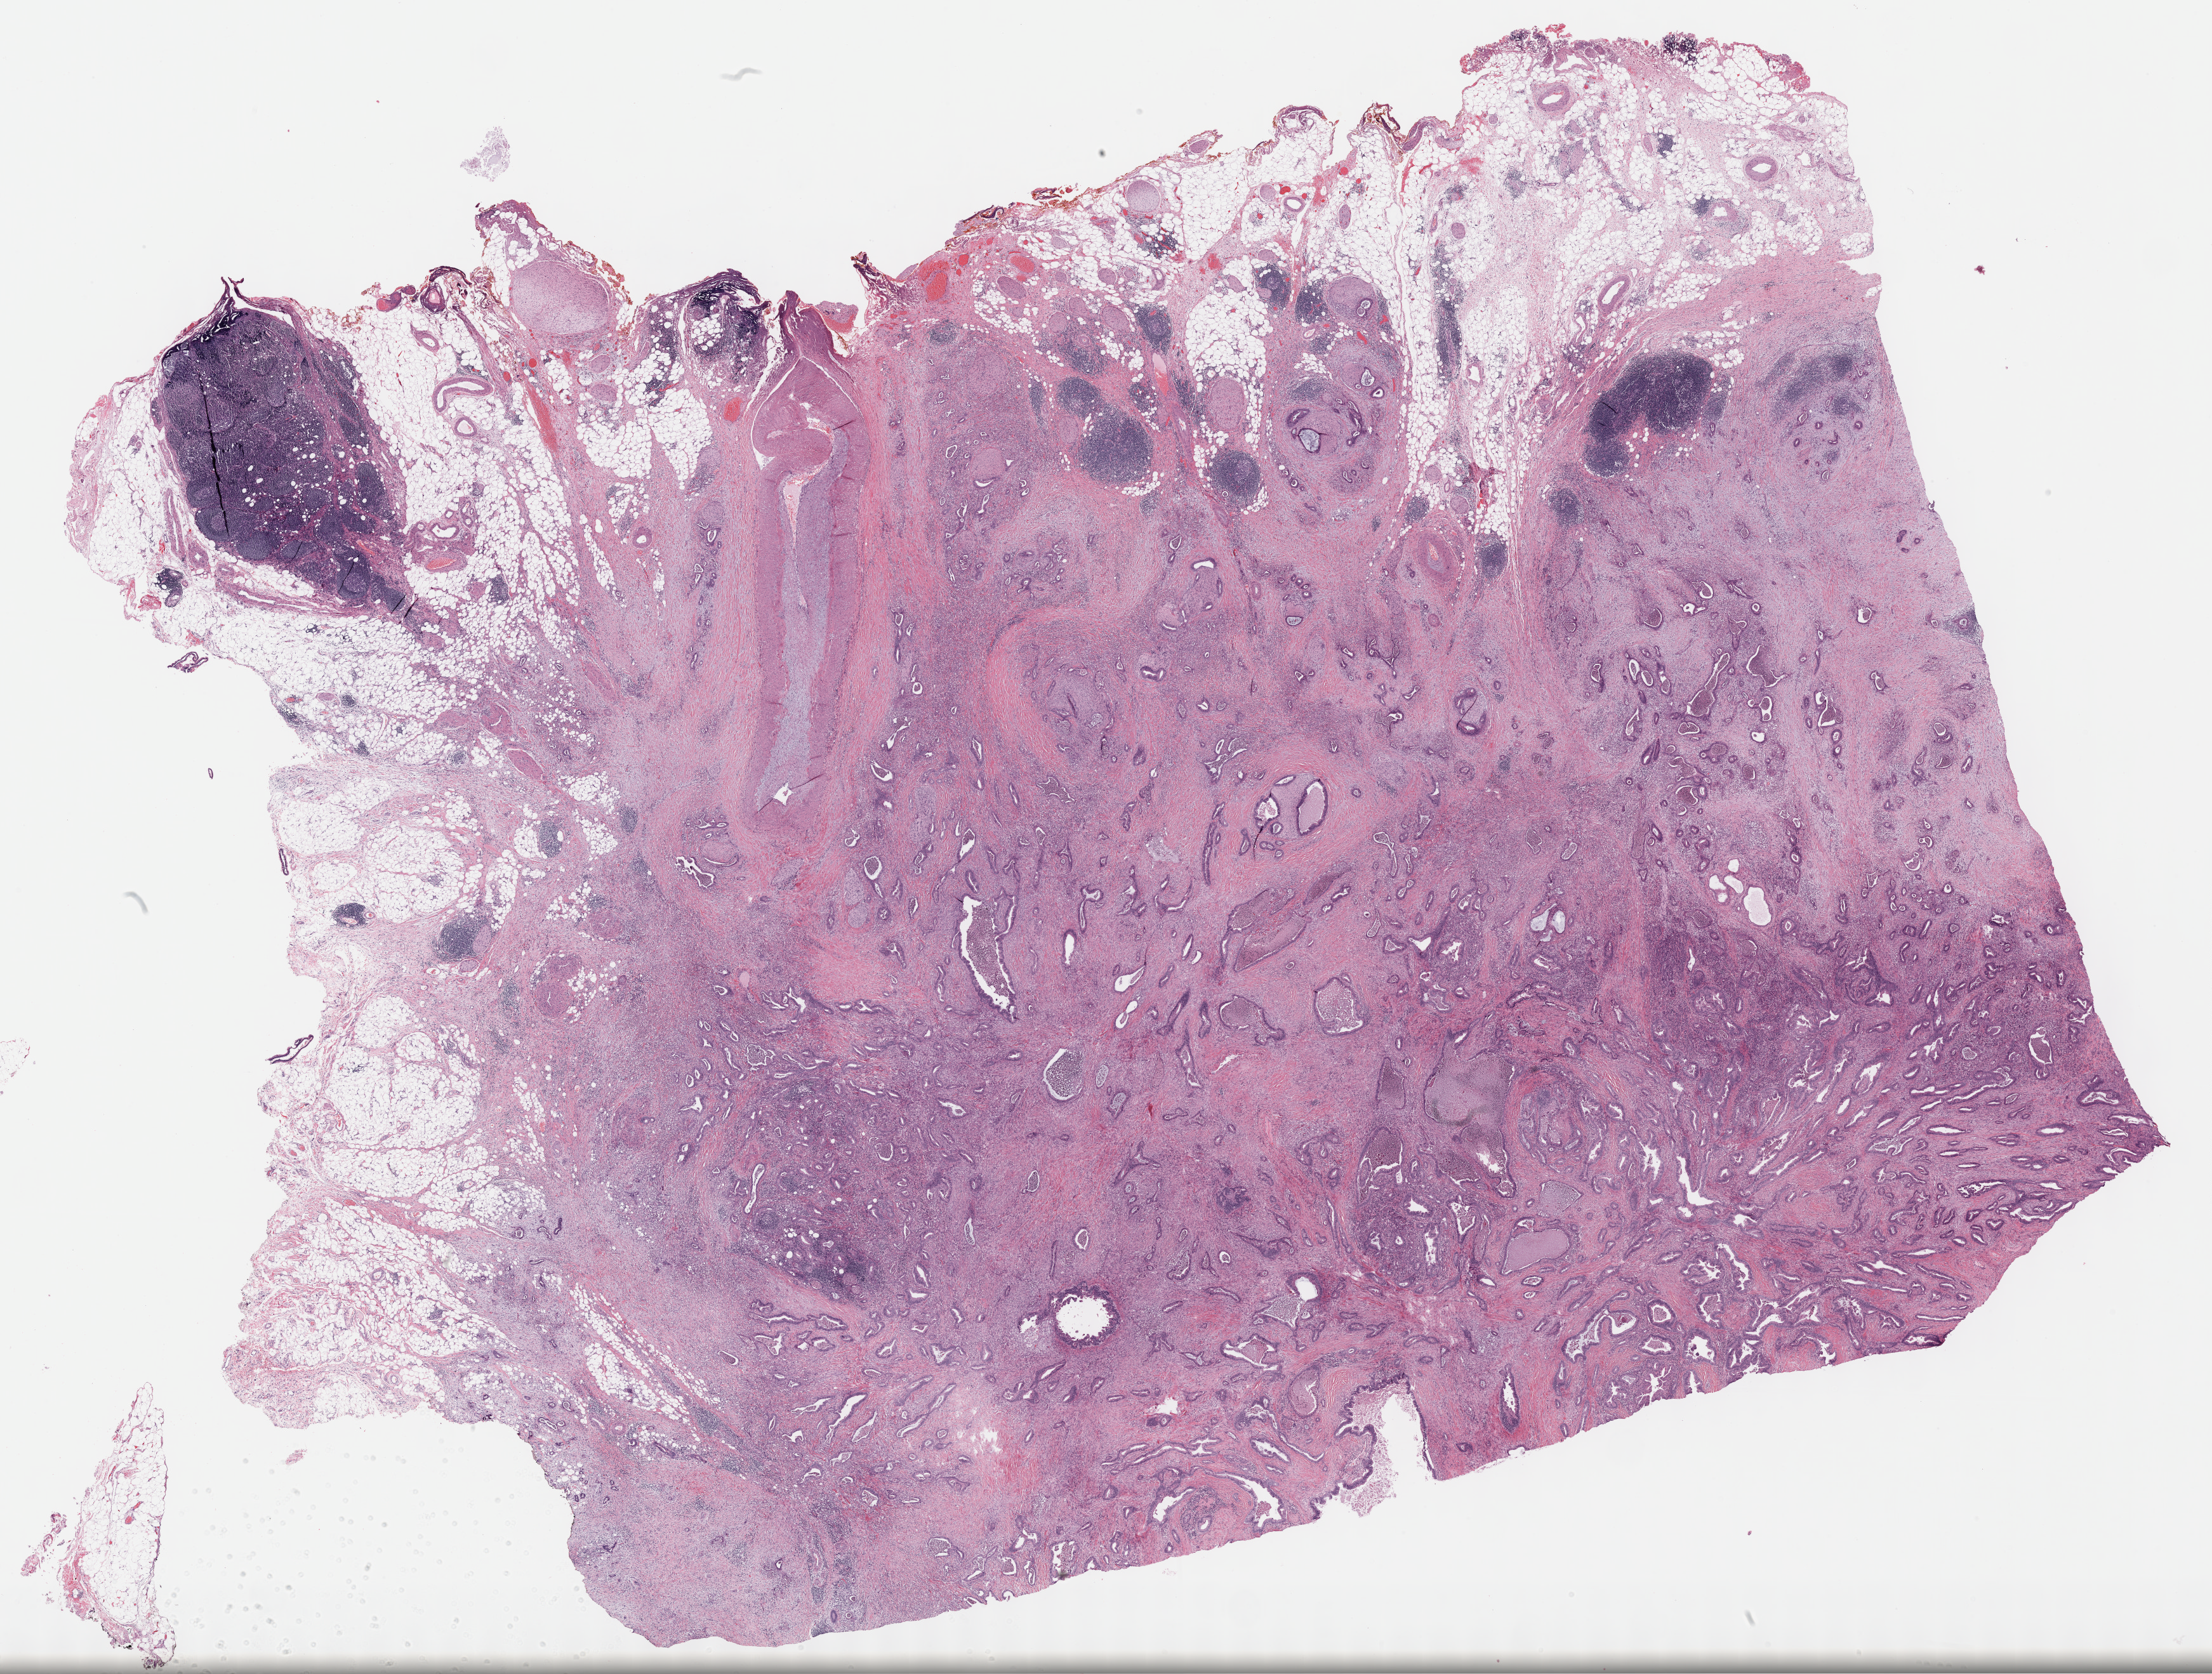
Digitized H&E tissue section (whole slide), a low-resolution overview of the entire scanned area, about 28.2 x 21.3 mm. Formalin-fixed paraffin-embedded (FFPE) diagnostic section. Primary tumour sample from the pancreas. Female, age 64 years at initial diagnosis. Histologic grade: G2 (moderately differentiated).
- lymph nodes positive (case pathology): 2 of 16 examined
- histologic diagnosis: Infiltrating duct carcinoma, NOS
- AJCC pathologic stage: IIB (7th edition)